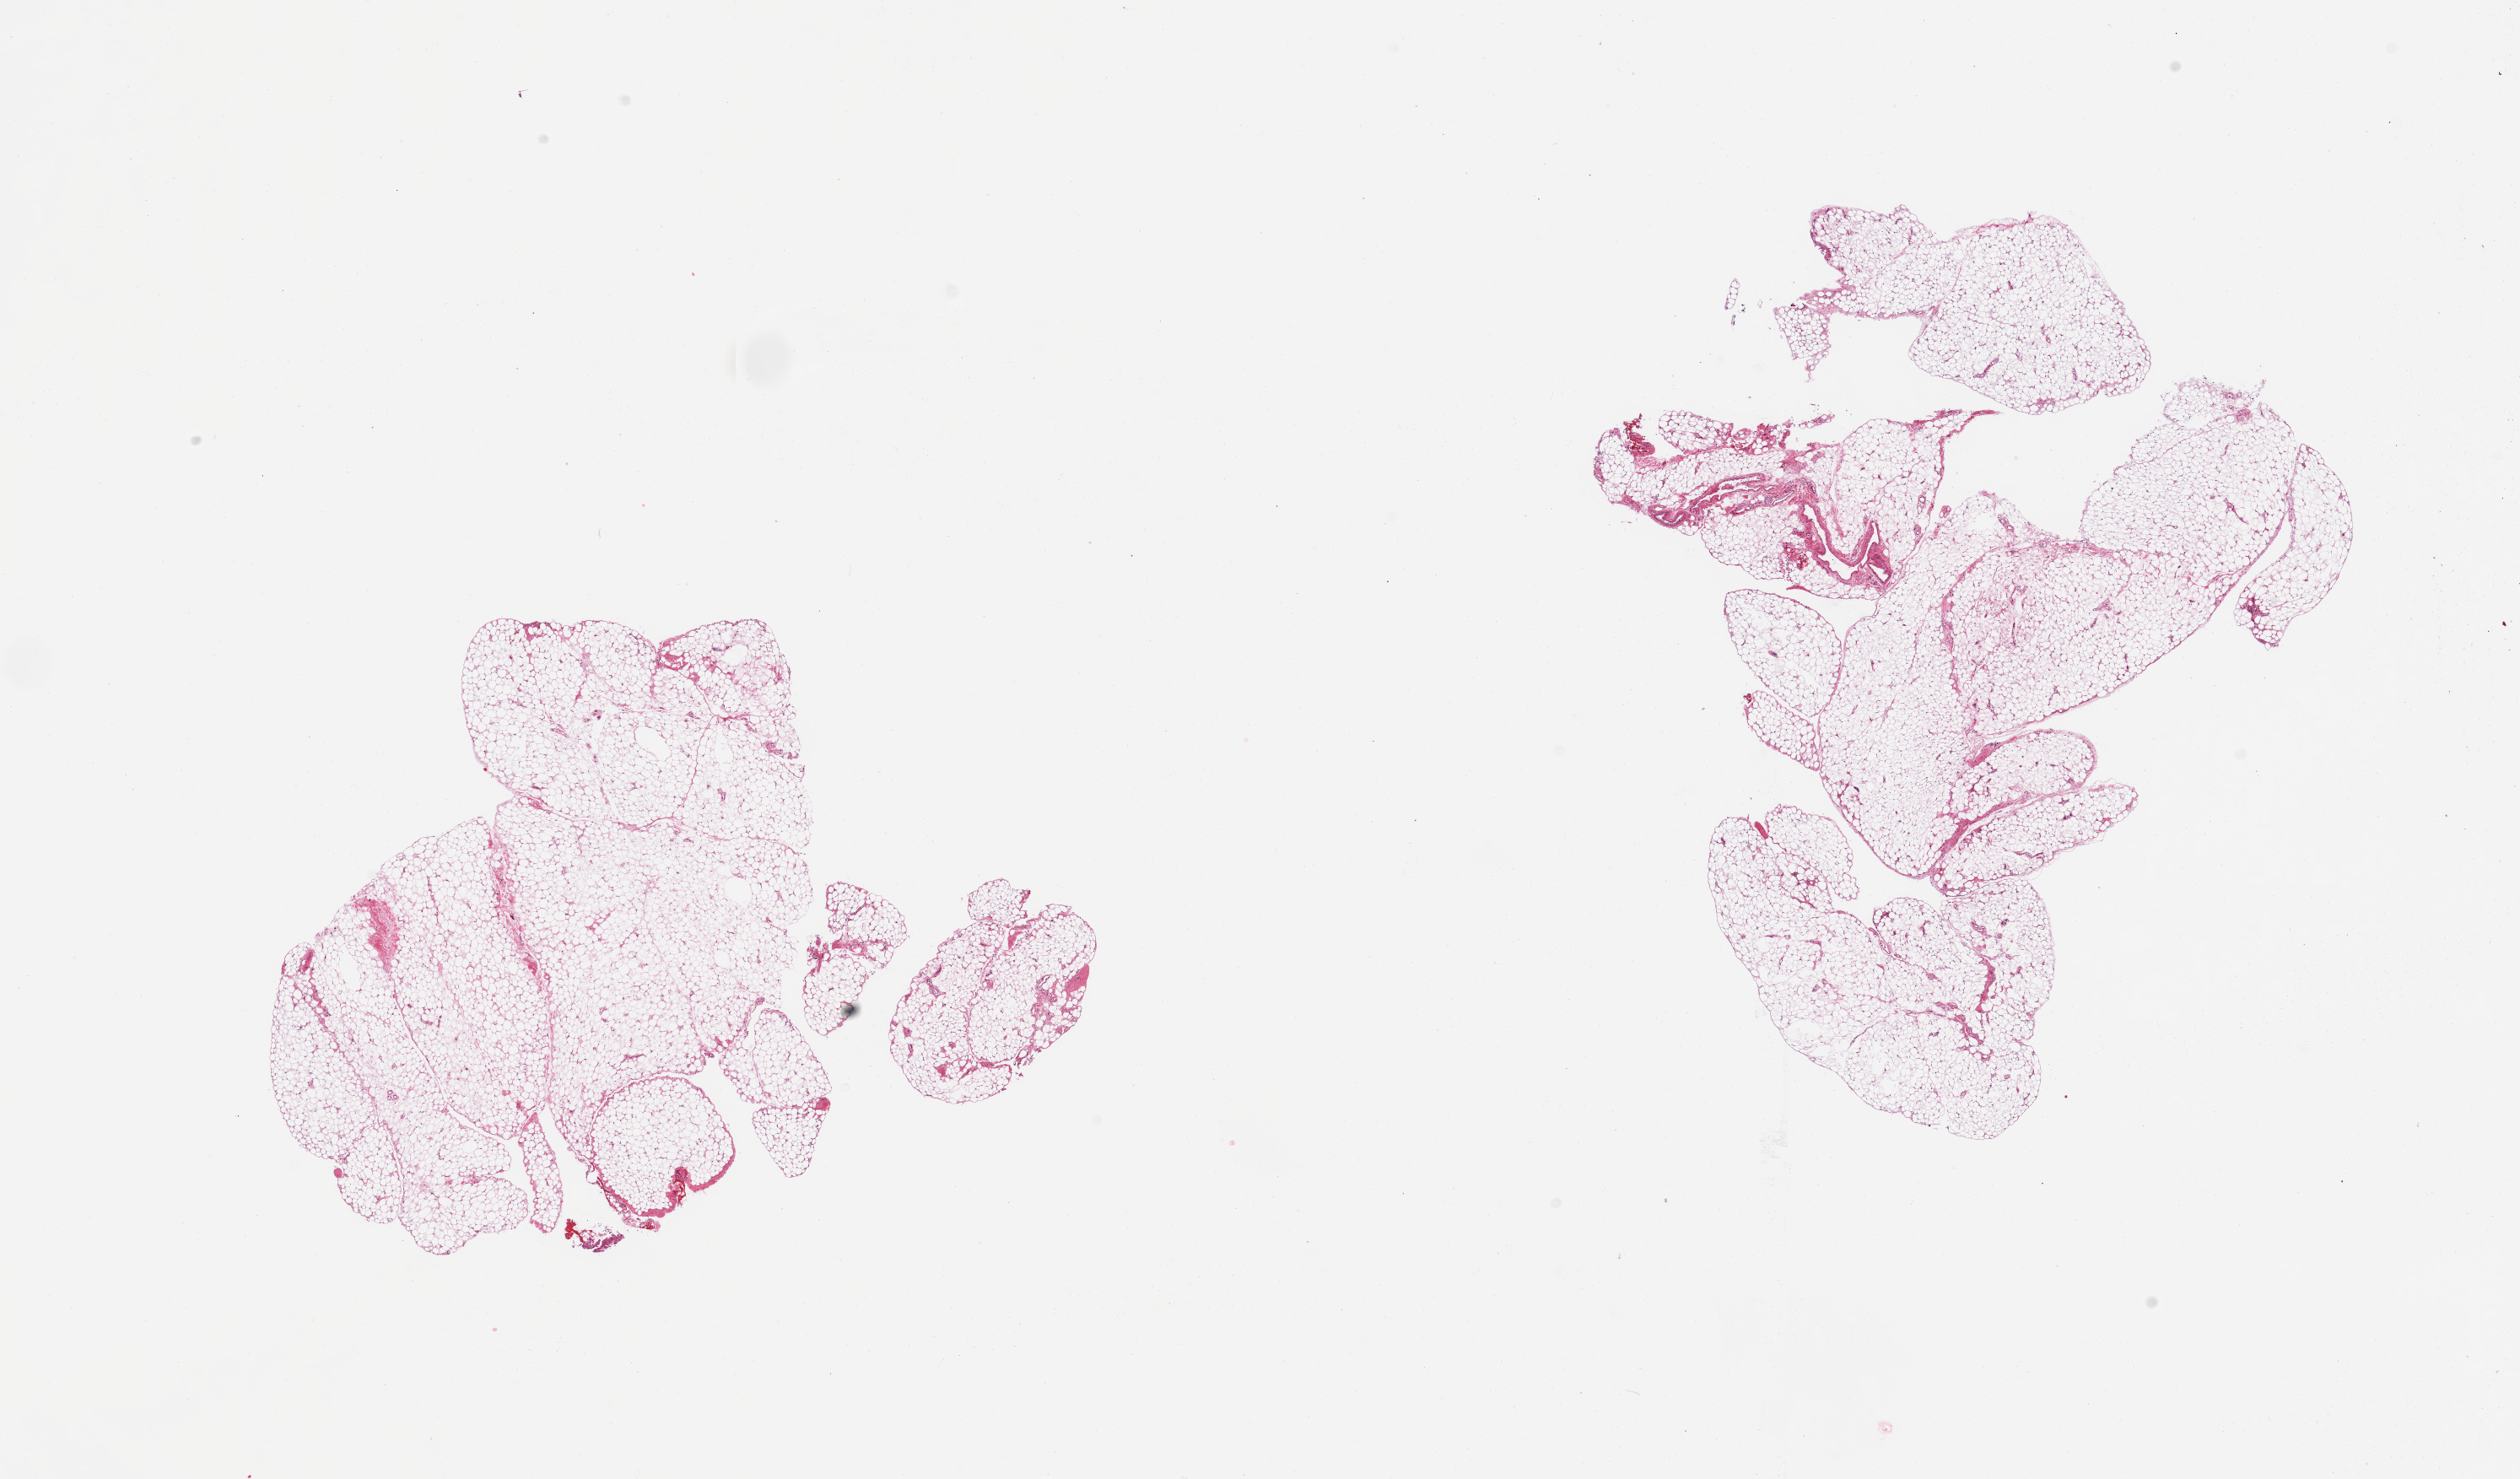
Digitized H&E-stained section — shown as a low-resolution overview of the whole scanned area (about 23.6 x 13.9 mm, acquisition: 20x scan); PAXgene-fixed, paraffin-embedded tissue; sampled site (target tissue): omentum; donor tissue sample. Donor: male.
Review note (as recorded): 2 pieces, ~5% interstitial vascular elements/fascia.